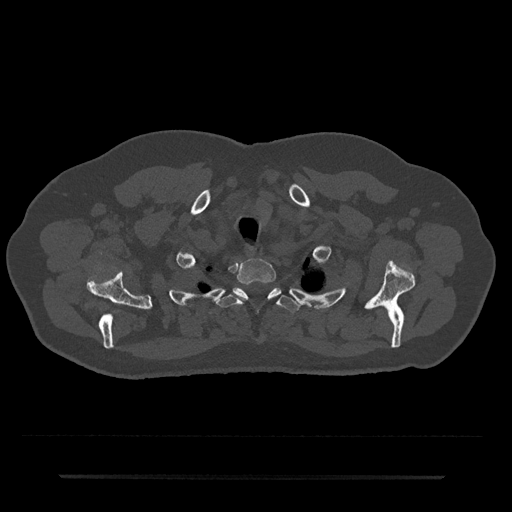
CT including the spine, one axial slice; slice 620 of 797 in the series (ordered by position); 120 kVp; bone window (W 1800 / L 400 HU); 512 × 512 image matrix, field of view 437 × 437 mm. Patient: male, 69 years. From the clinical record (not read from this slice): primary cancer: prostate.
Outlined on this slice (semi-automatically segmented with operator editing):
- T1 vertebra: bounding box [x1, y1, x2, y2] px = [237, 259, 276, 285]
- T2 vertebra: [219, 287, 299, 313]